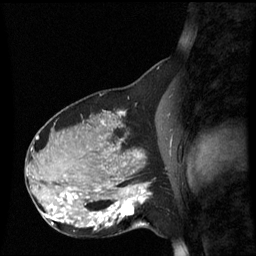
Breast MRI (dynamic contrast-enhanced), one sagittal slice; slice 30 of 60 in the series (ordered by position); dynamic contrast-enhanced series, image 2 of 3 at this slice position (ordered by acquisition); 1.5 T; TE 4.2 ms, TR 8.9 ms; 2.2 mm slice thickness; 256 × 256 image matrix, field of view 220 × 220 mm. Female patient, age 31 years. From the clinical record (not read from this slice): setting: breast cancer imaged before/during neoadjuvant chemotherapy; receptor status: HR-positive, HER2-negative.
Annotated regions visible in this slice (semi-automatic segmentation, software-assisted and operator-edited):
- analysis volume of interest (the breast-tissue region the enhancement analysis was run in; not a lesion): box from (x=90, y=180) to (x=152, y=235) px
- tumour enhancement mask (voxels above the 70 % enhancement threshold inside the analysis volume of interest): (x=90, y=184)–(x=151, y=227)